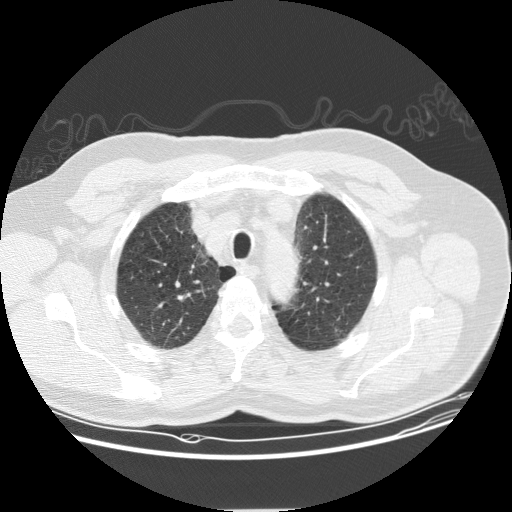
Axial slice from a low-dose chest CT screening exam; first (baseline) screen; lung window (W 1500 / L -600 HU); slice 30 of 157 in the series; 512 × 512 image matrix, field of view 400 × 400 mm. Male participant, aged 61 years at enrolment.
- Expert reader's lesion annotation, bounding box (x1, y1, x2, y2) in pixels: (158, 284, 196, 320).
- No non-calcified nodule or mass ≥4 mm was recorded by the screening reader at this exam.
- Later outcome: lung cancer diagnosed 832 days after this screen (after the third annual screen) — squamous cell carcinoma, NOS, right upper lobe, moderately differentiated (G2), stage IA (AJCC 6th edition), 10 mm at pathology.